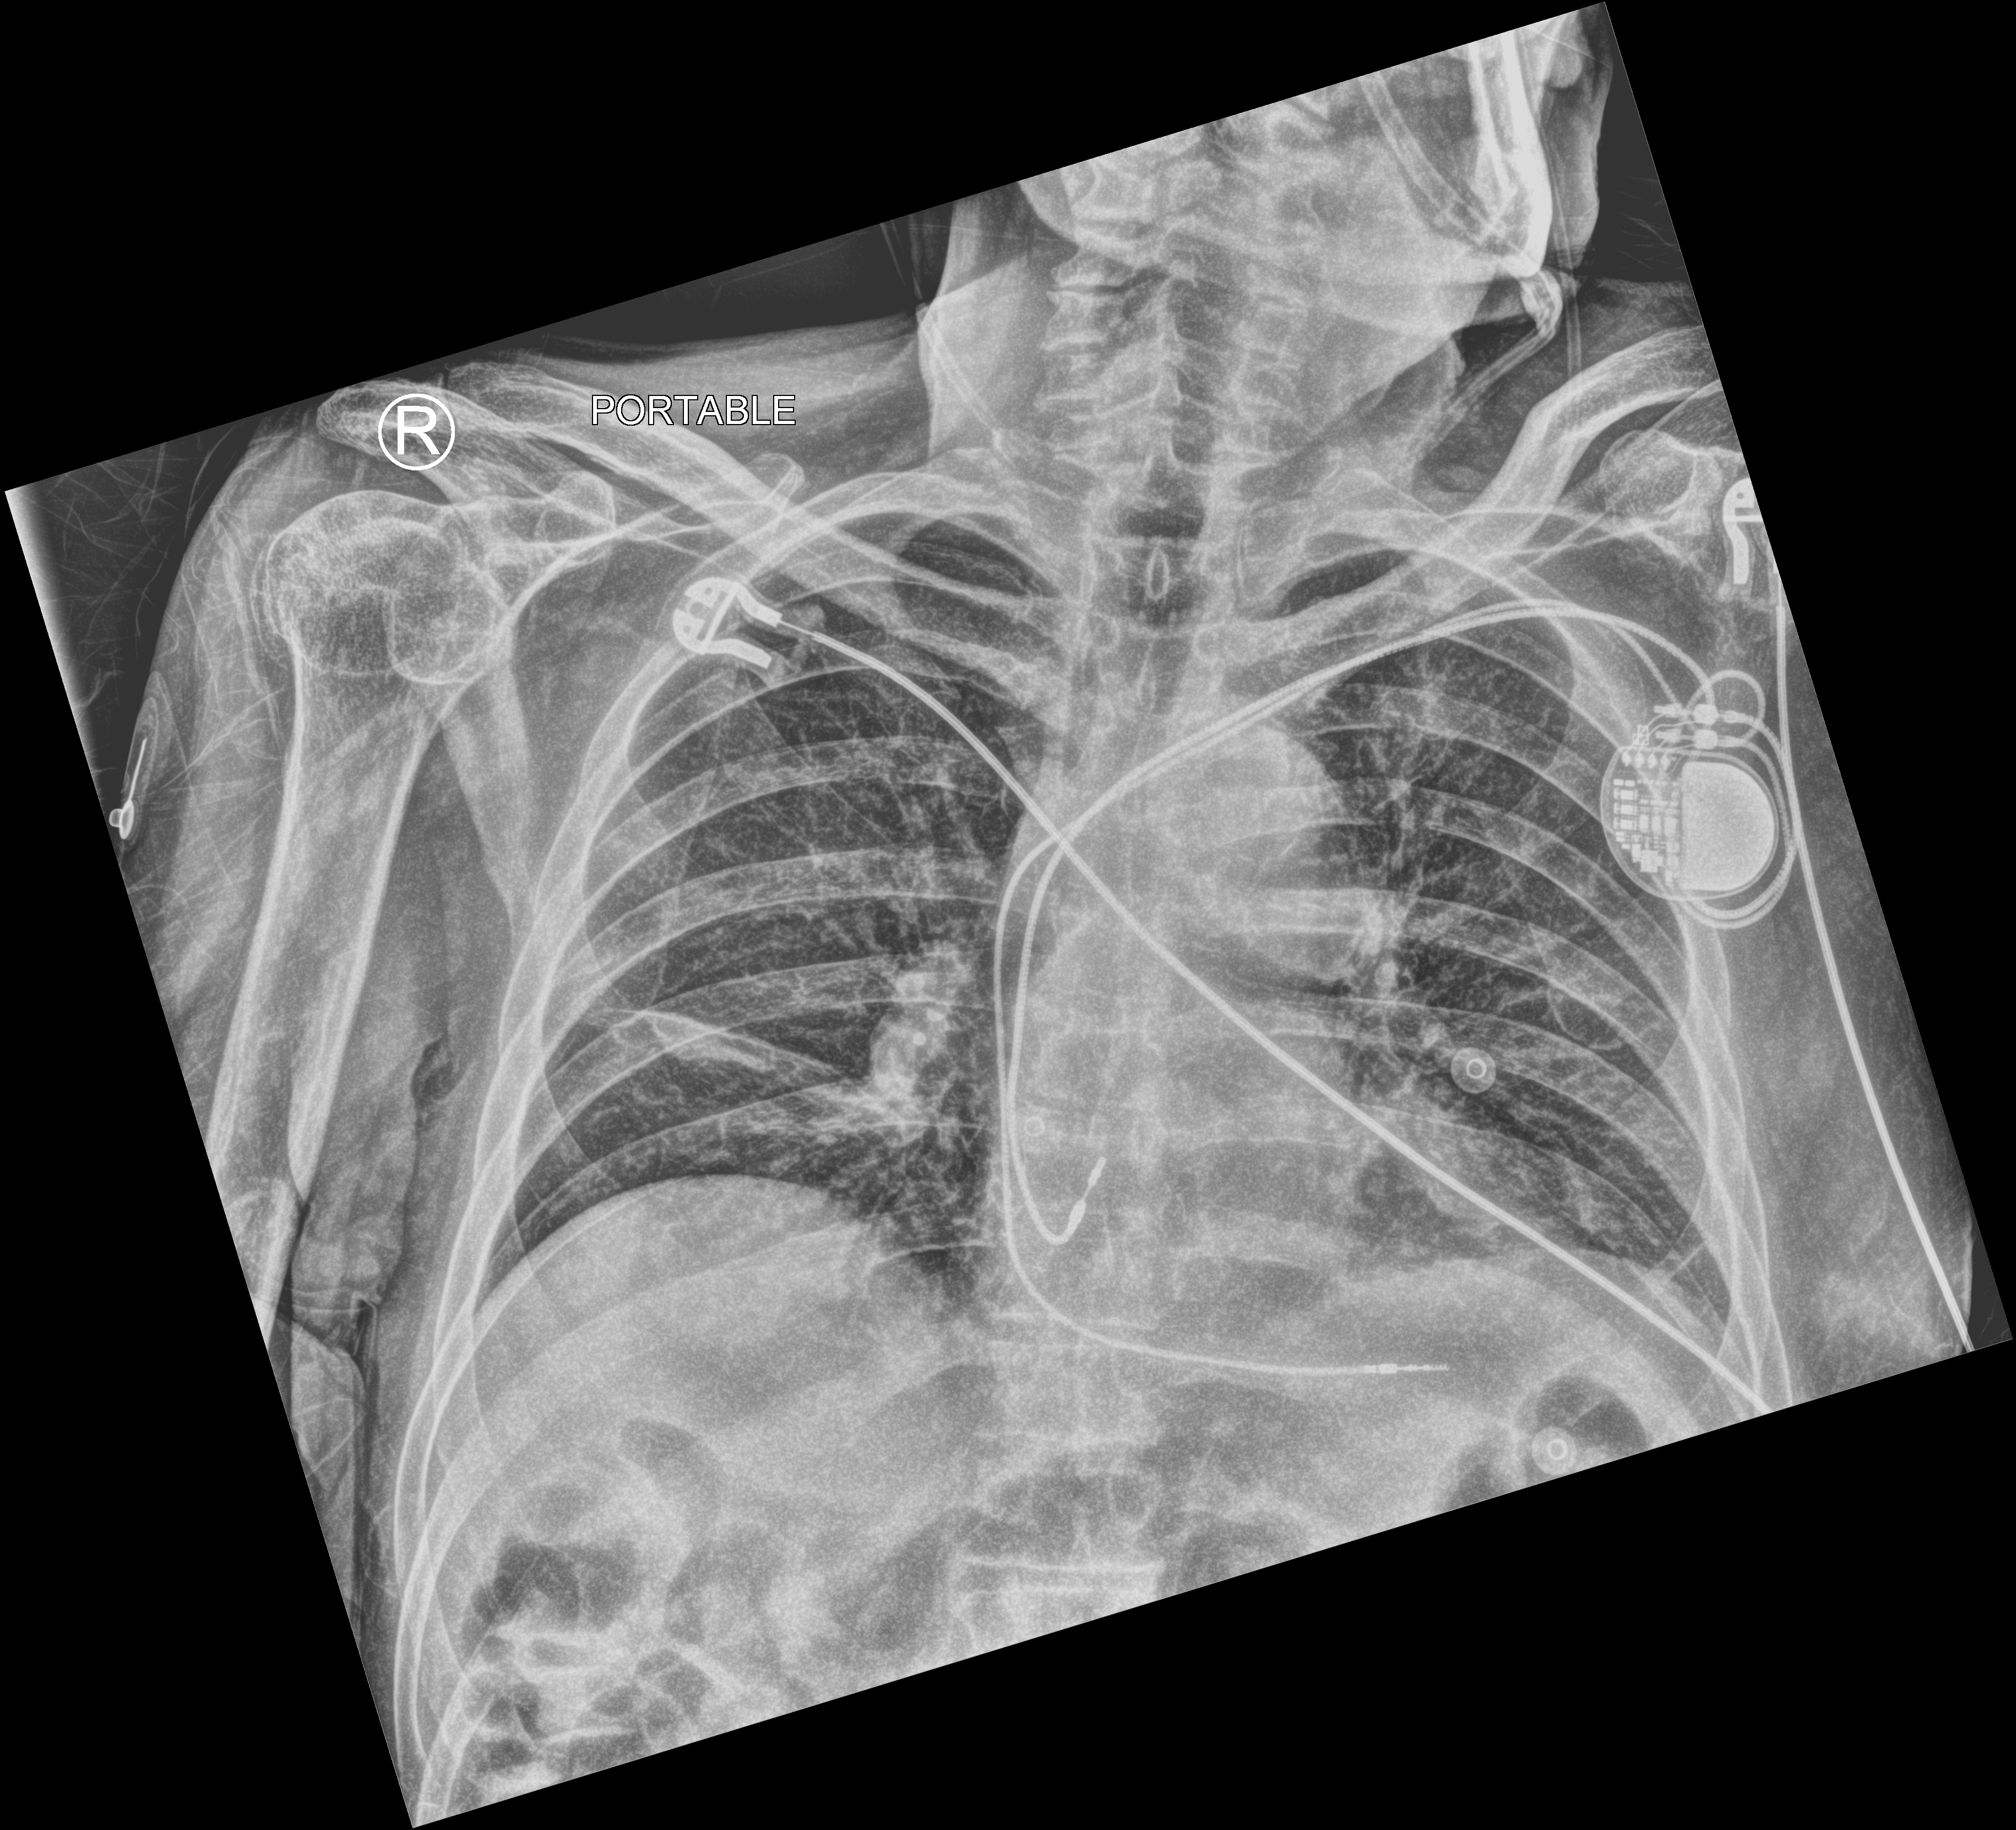
Bedside chest radiograph (computed radiography), anteroposterior (AP) projection. Male patient hospitalised with COVID-19, age 60–74 years.
Admission-level facts for this patient (not findings on this image; timing relative to this image not recorded): length of hospital stay: 6 days.